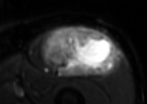
MRI of an extremity soft-tissue mass, one axial slice; slice 53 of 85 in the series (ordered by position); T2-weighted fat-saturated; MR volume resampled by the dataset authors to the PET/CT grid (not the native acquisition matrix); 3.27 mm slice thickness; 147 × 104 image matrix. Male patient. From the clinical record (not read from this slice): histological type: extraskeletal osteosarcoma; grade: high; site of the primary tumour: thigh.
Structures marked on this image (expert contour drawn on MRI and transferred to this co-registered scan by the dataset authors):
- gross tumour volume (mass): bounding box <40,26,116,77> (left, top, right, bottom; pixels)